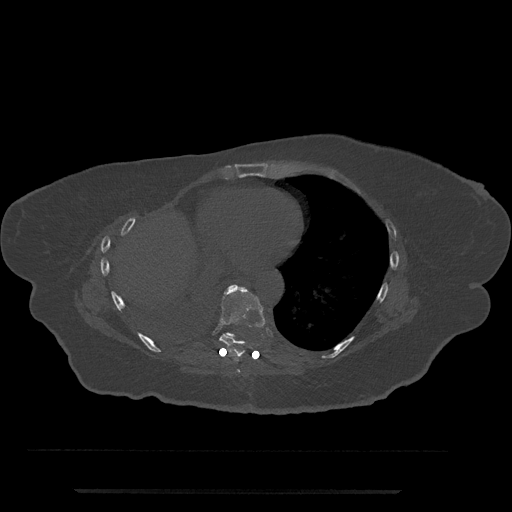
CT including the spine, one axial slice. Slice 381 of 797 in the series (ordered by position). Reconstruction kernel Br40s/3. 120 kVp. Bone window (W 1800 / L 400 HU). 512 × 512 image matrix, field of view 440 × 440 mm. Patient: female, 51 years. From the clinical record (not read from this slice): primary cancer: neuro; vertebrae with lytic lesions (as recorded): T8.
Outlined on this slice (semi-automatically segmented with operator editing):
- T7 vertebra: bounding box [x1, y1, x2, y2] px = [236, 369, 241, 373]
- T8 vertebra: [219, 284, 265, 358]
- T9 vertebra: [226, 287, 264, 340]